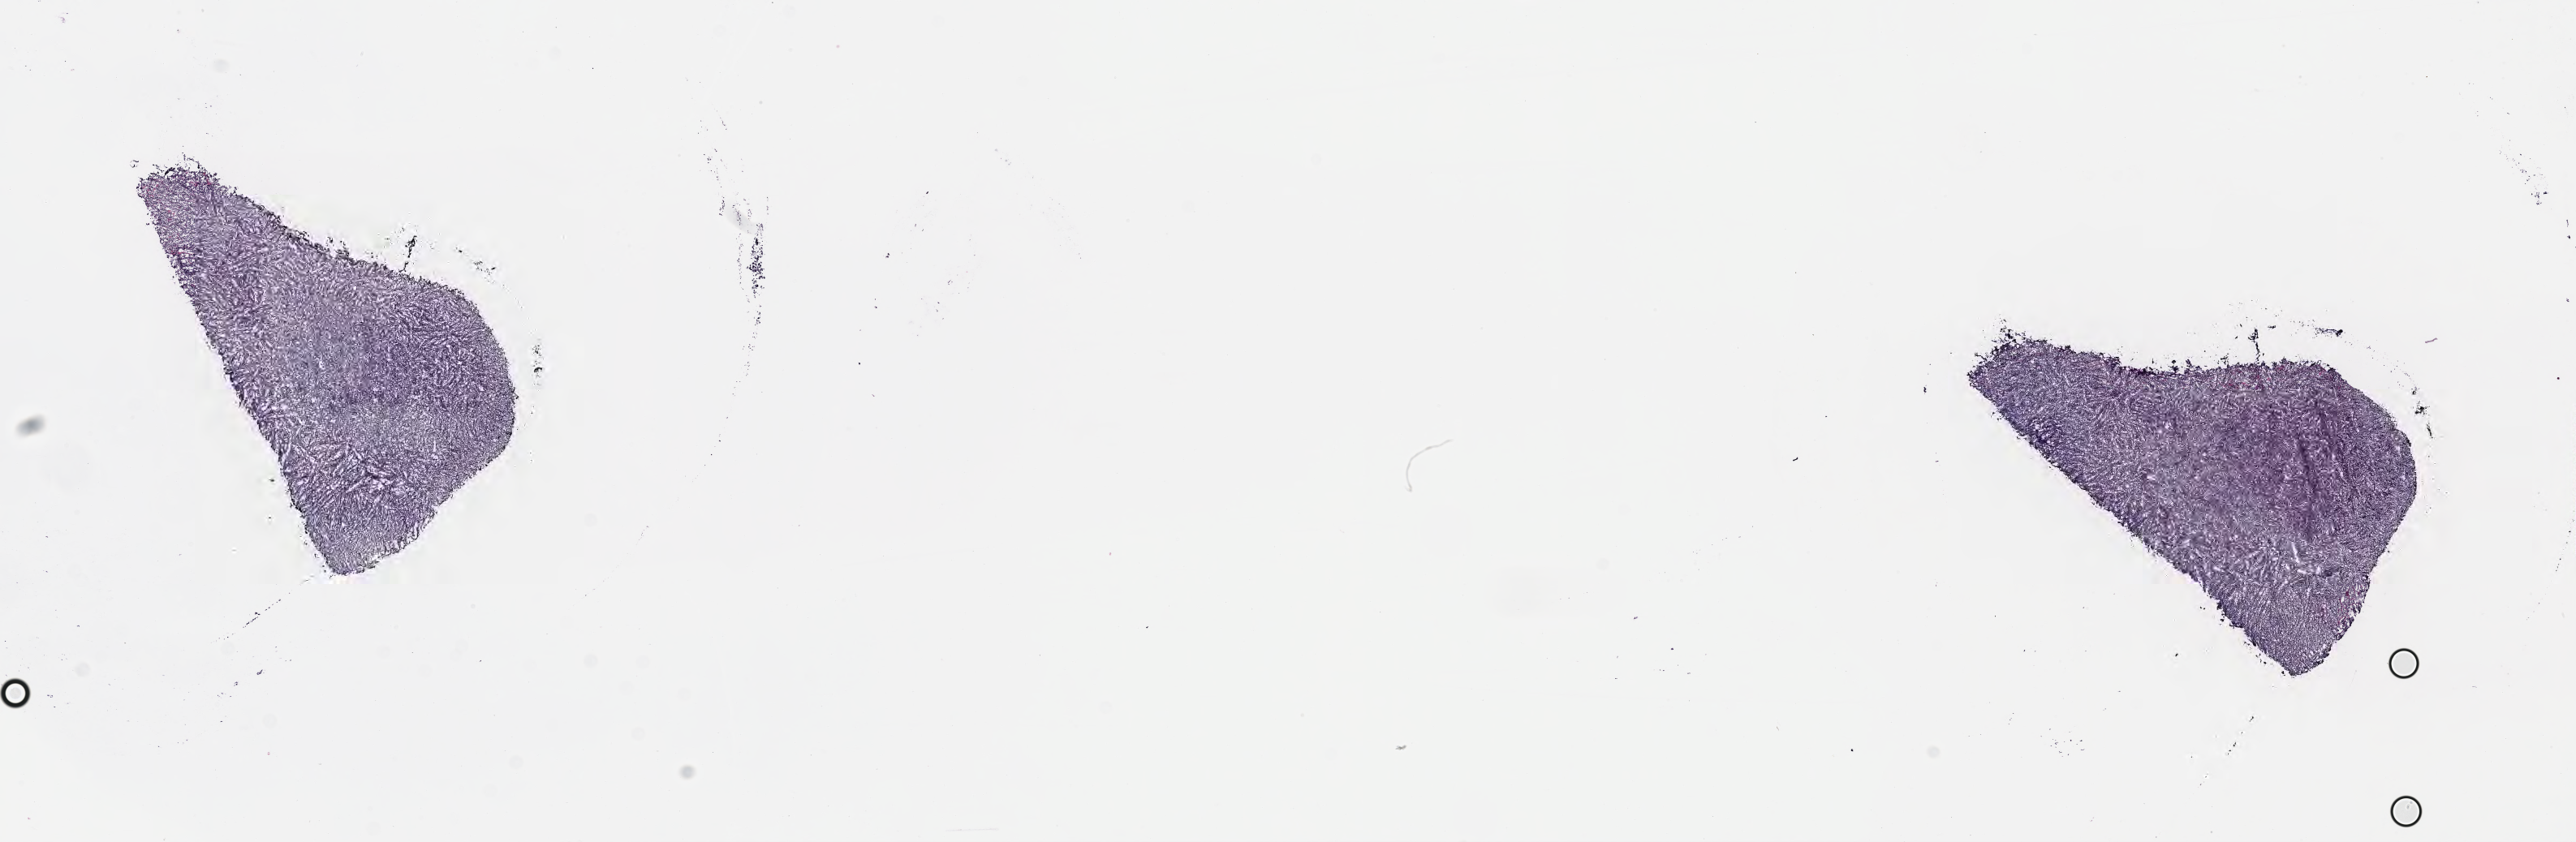
H&E whole-slide image — a low-resolution overview of the entire scanned area, about 25.7 x 8.4 mm, frozen section (tissue freezing medium), specimen: primary tumor, site: lymph node of head and neck. Male, age 6 years at initial diagnosis. Composition of this section per pathologist review: tumor cells 95%, tumor nuclei 95%.
Histologic diagnosis: Burkitt lymphoma, NOS.